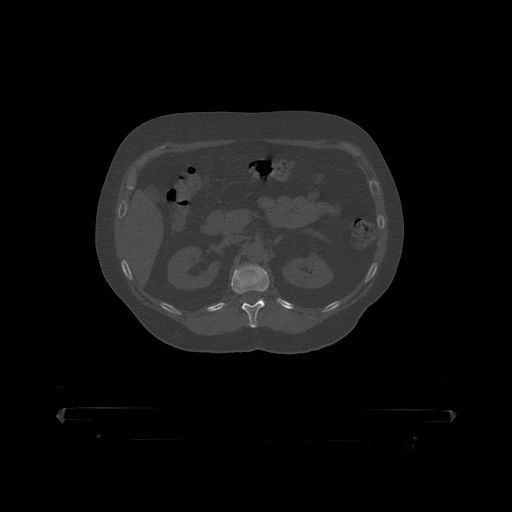
CT including the spine, one axial slice; slice 163 of 390 in the series (ordered by position); reconstruction kernel STANDARD; bone window (W 1800 / L 400 HU); 1.25 mm slice thickness; 512 × 512 image matrix. Male patient, age 60 years. From the clinical record (not read from this slice): primary cancer: prostate.
Structures marked on this image (semi-automatic segmentation, software-assisted and operator-edited):
- T12 vertebra: bounding box [x1, y1, x2, y2] px = [232, 264, 270, 319]